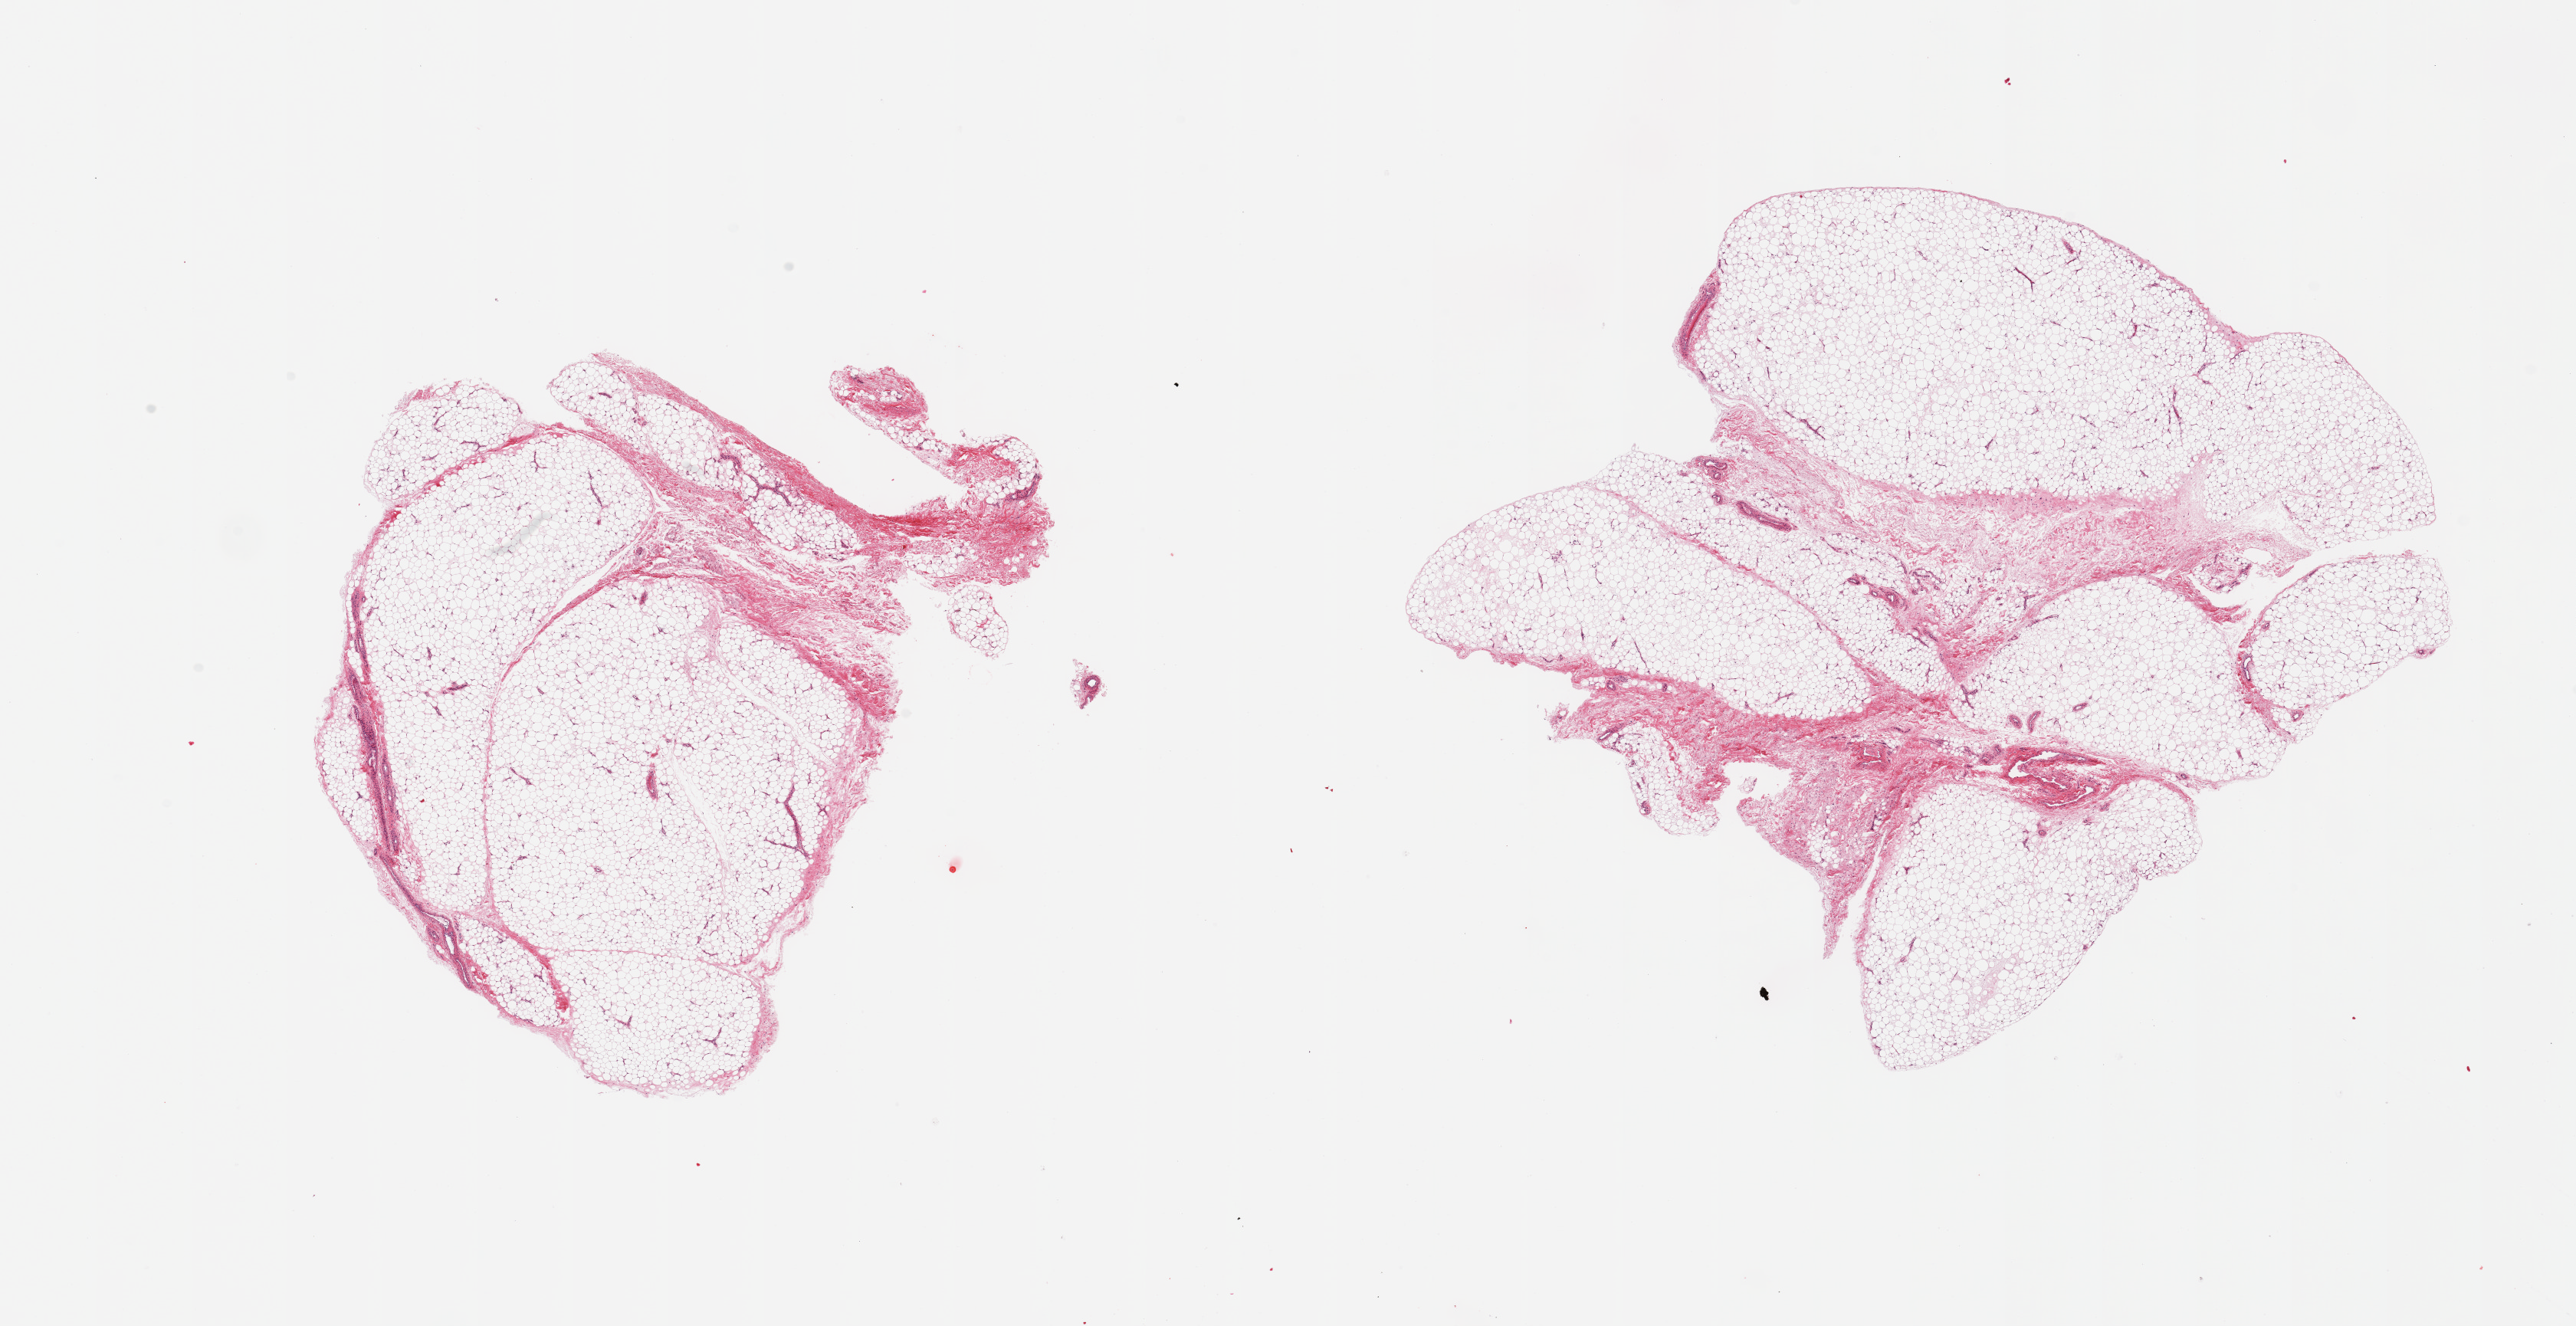
Digitized hematoxylin and eosin (H&E)-stained section, brightfield — shown as a low-resolution overview of the whole scanned area (about 26.6 x 13.7 mm); PAXgene-fixed paraffin-embedded (PFPE) section; section of adipose tissue (target tissue); donor tissue sample. Donor: male.
Review note (as recorded): 2 pieces, fascia/vascular elements are ~15% tissue.